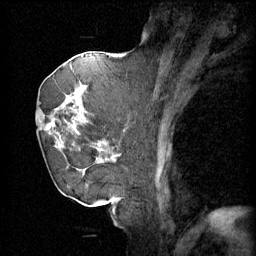
Breast MRI (dynamic contrast-enhanced), one sagittal slice; position 25 of 60 along the scan axis; 4 images stored at this slice position (order not interpretable as contrast timing); 1.5 T; TE 4.2 ms, TR 11 ms; 256 × 256 image matrix, field of view 220 × 220 mm. Patient: female, 72 years.
Outlined on this slice (semi-automatically segmented with operator editing):
- analysis volume of interest (the breast-tissue region the enhancement analysis was run in; not a lesion): box from (x=43, y=68) to (x=109, y=163) px
- tumour enhancement mask (voxels above the 70 % enhancement threshold inside the analysis volume of interest): (x=43, y=84)–(x=109, y=163)